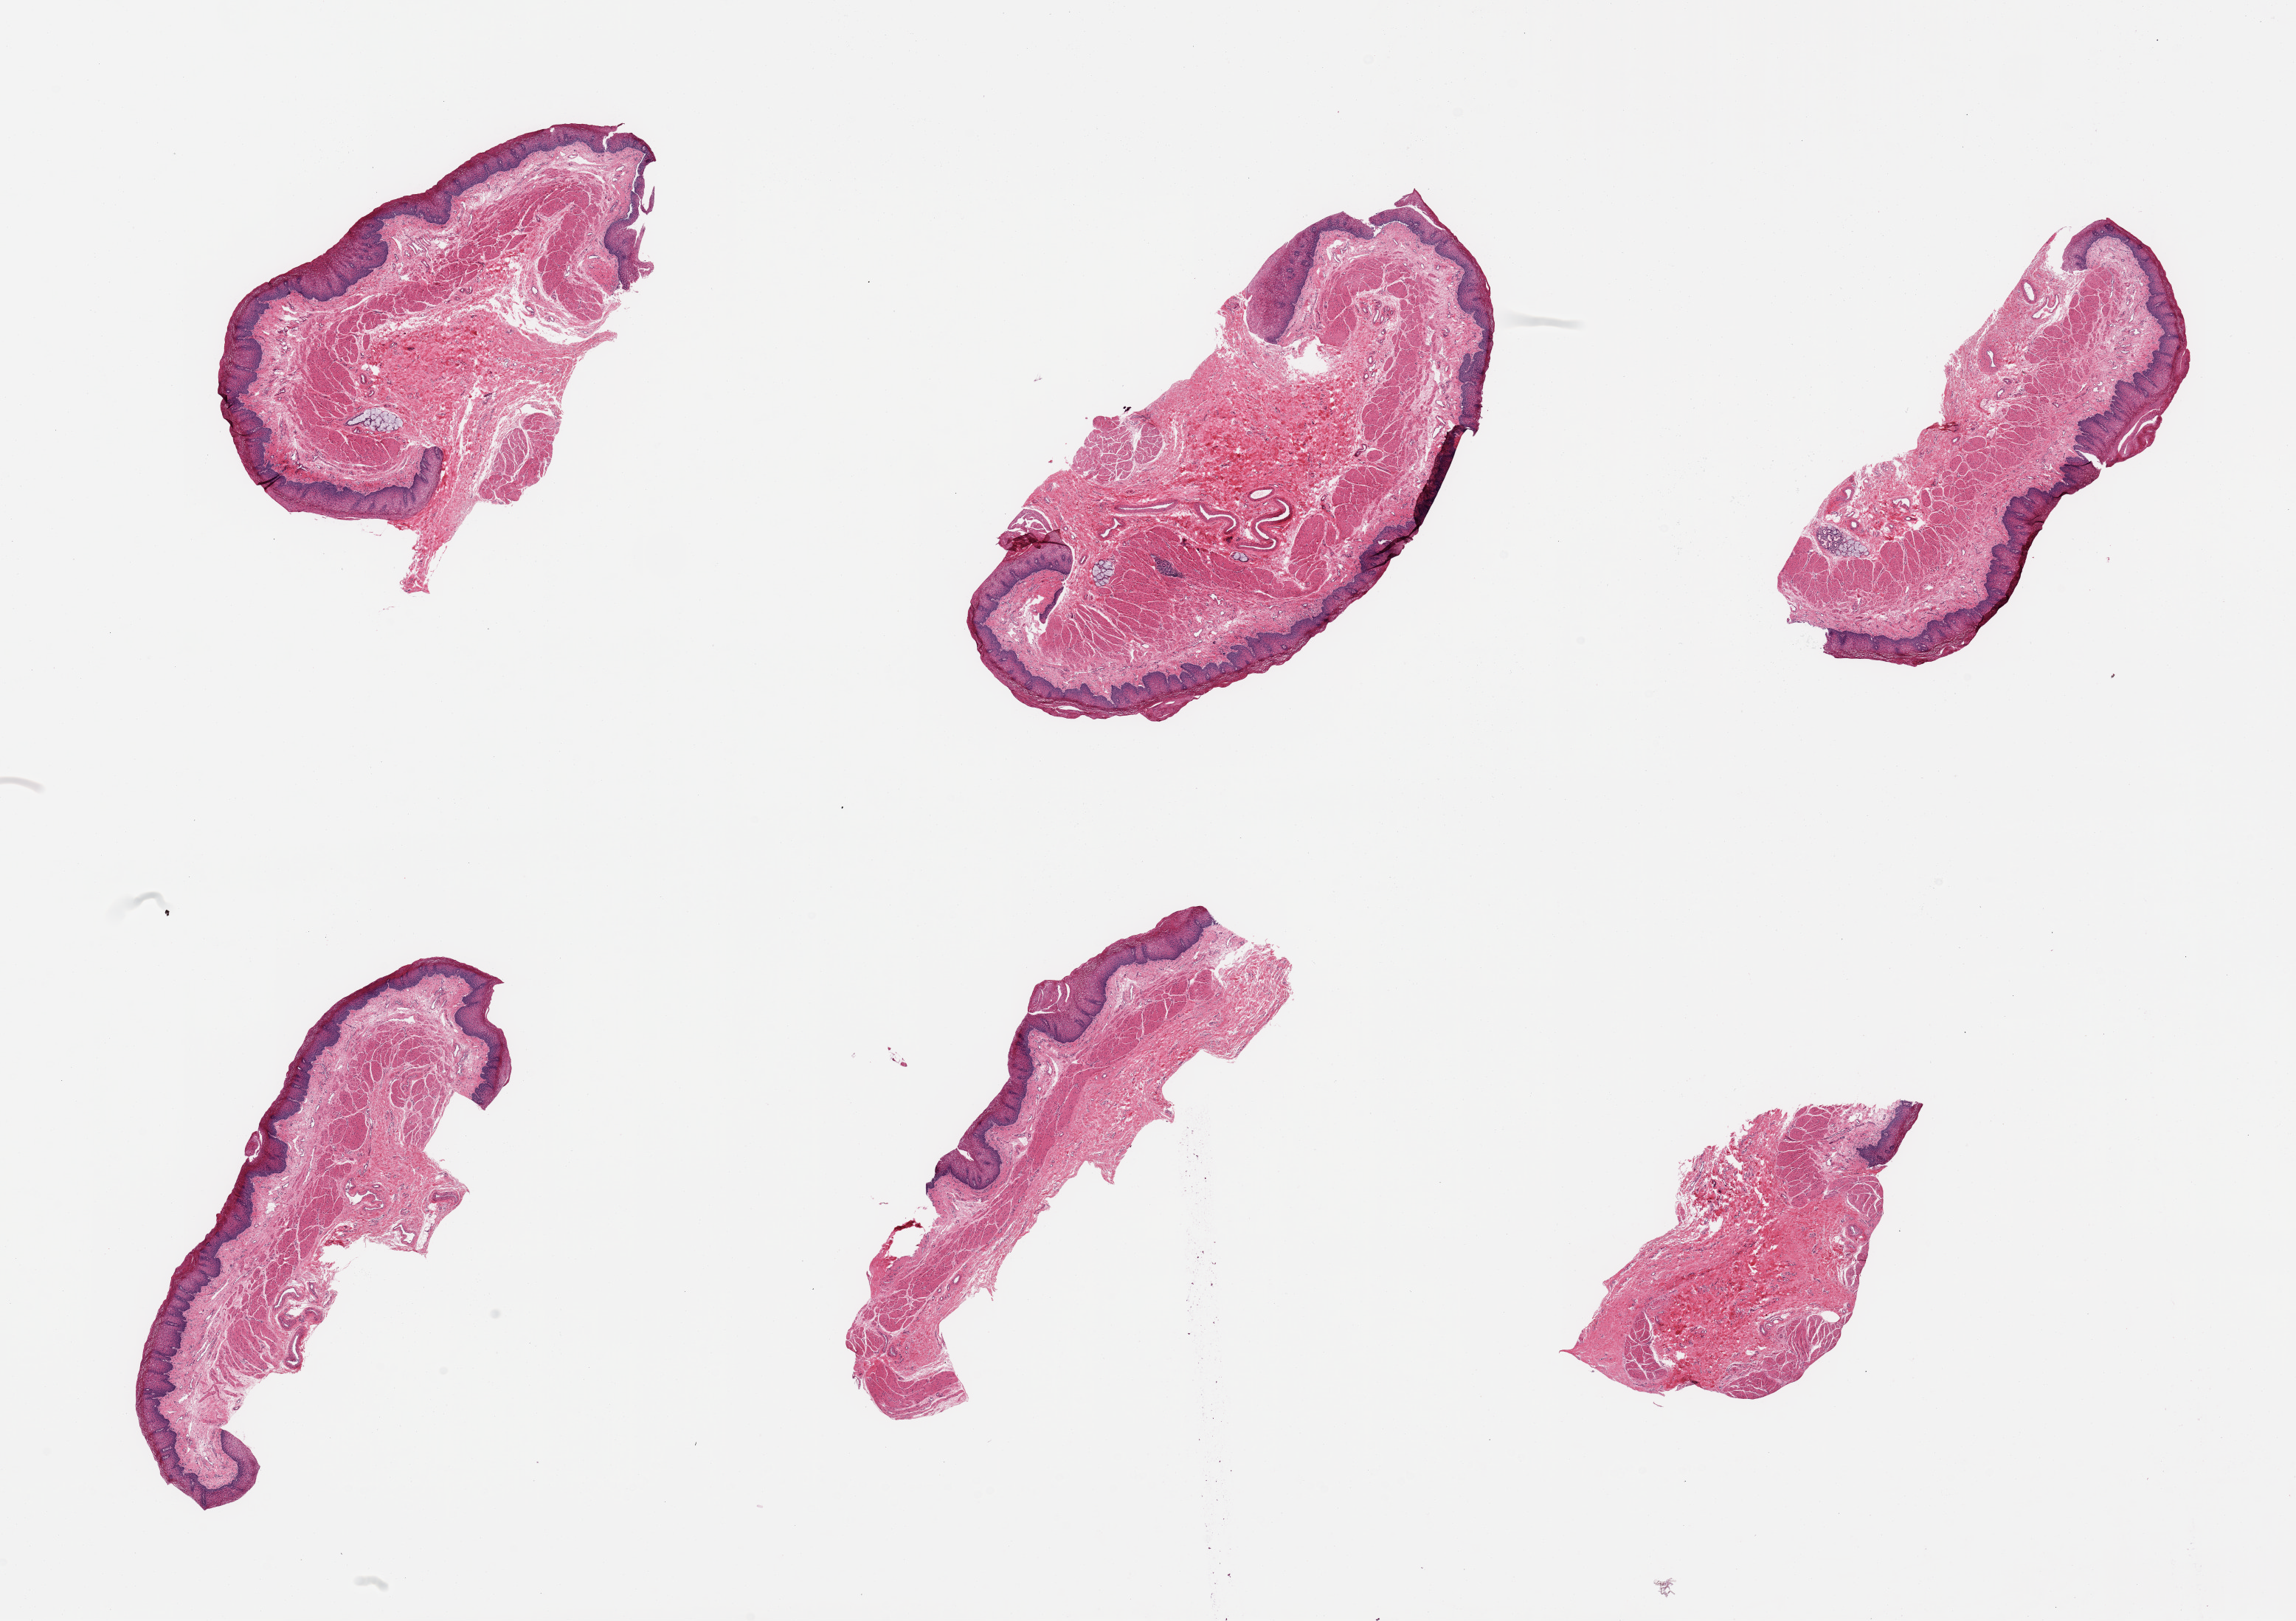
Digitized haematoxylin and eosin-stained section — low-resolution overview of the scanned area, about 24.6 x 17.4 mm, PAXgene-fixed paraffin-embedded (PFPE) section, section of esophageal mucous membrane (target tissue), donor tissue sample.
• review note (as recorded): 6 pieces; predominantly mucosa, muscularis mucosae, submucosa, with few submucosal glands and rare portion of muscularis propria, some squamous hyperplasia suggestive of reflux